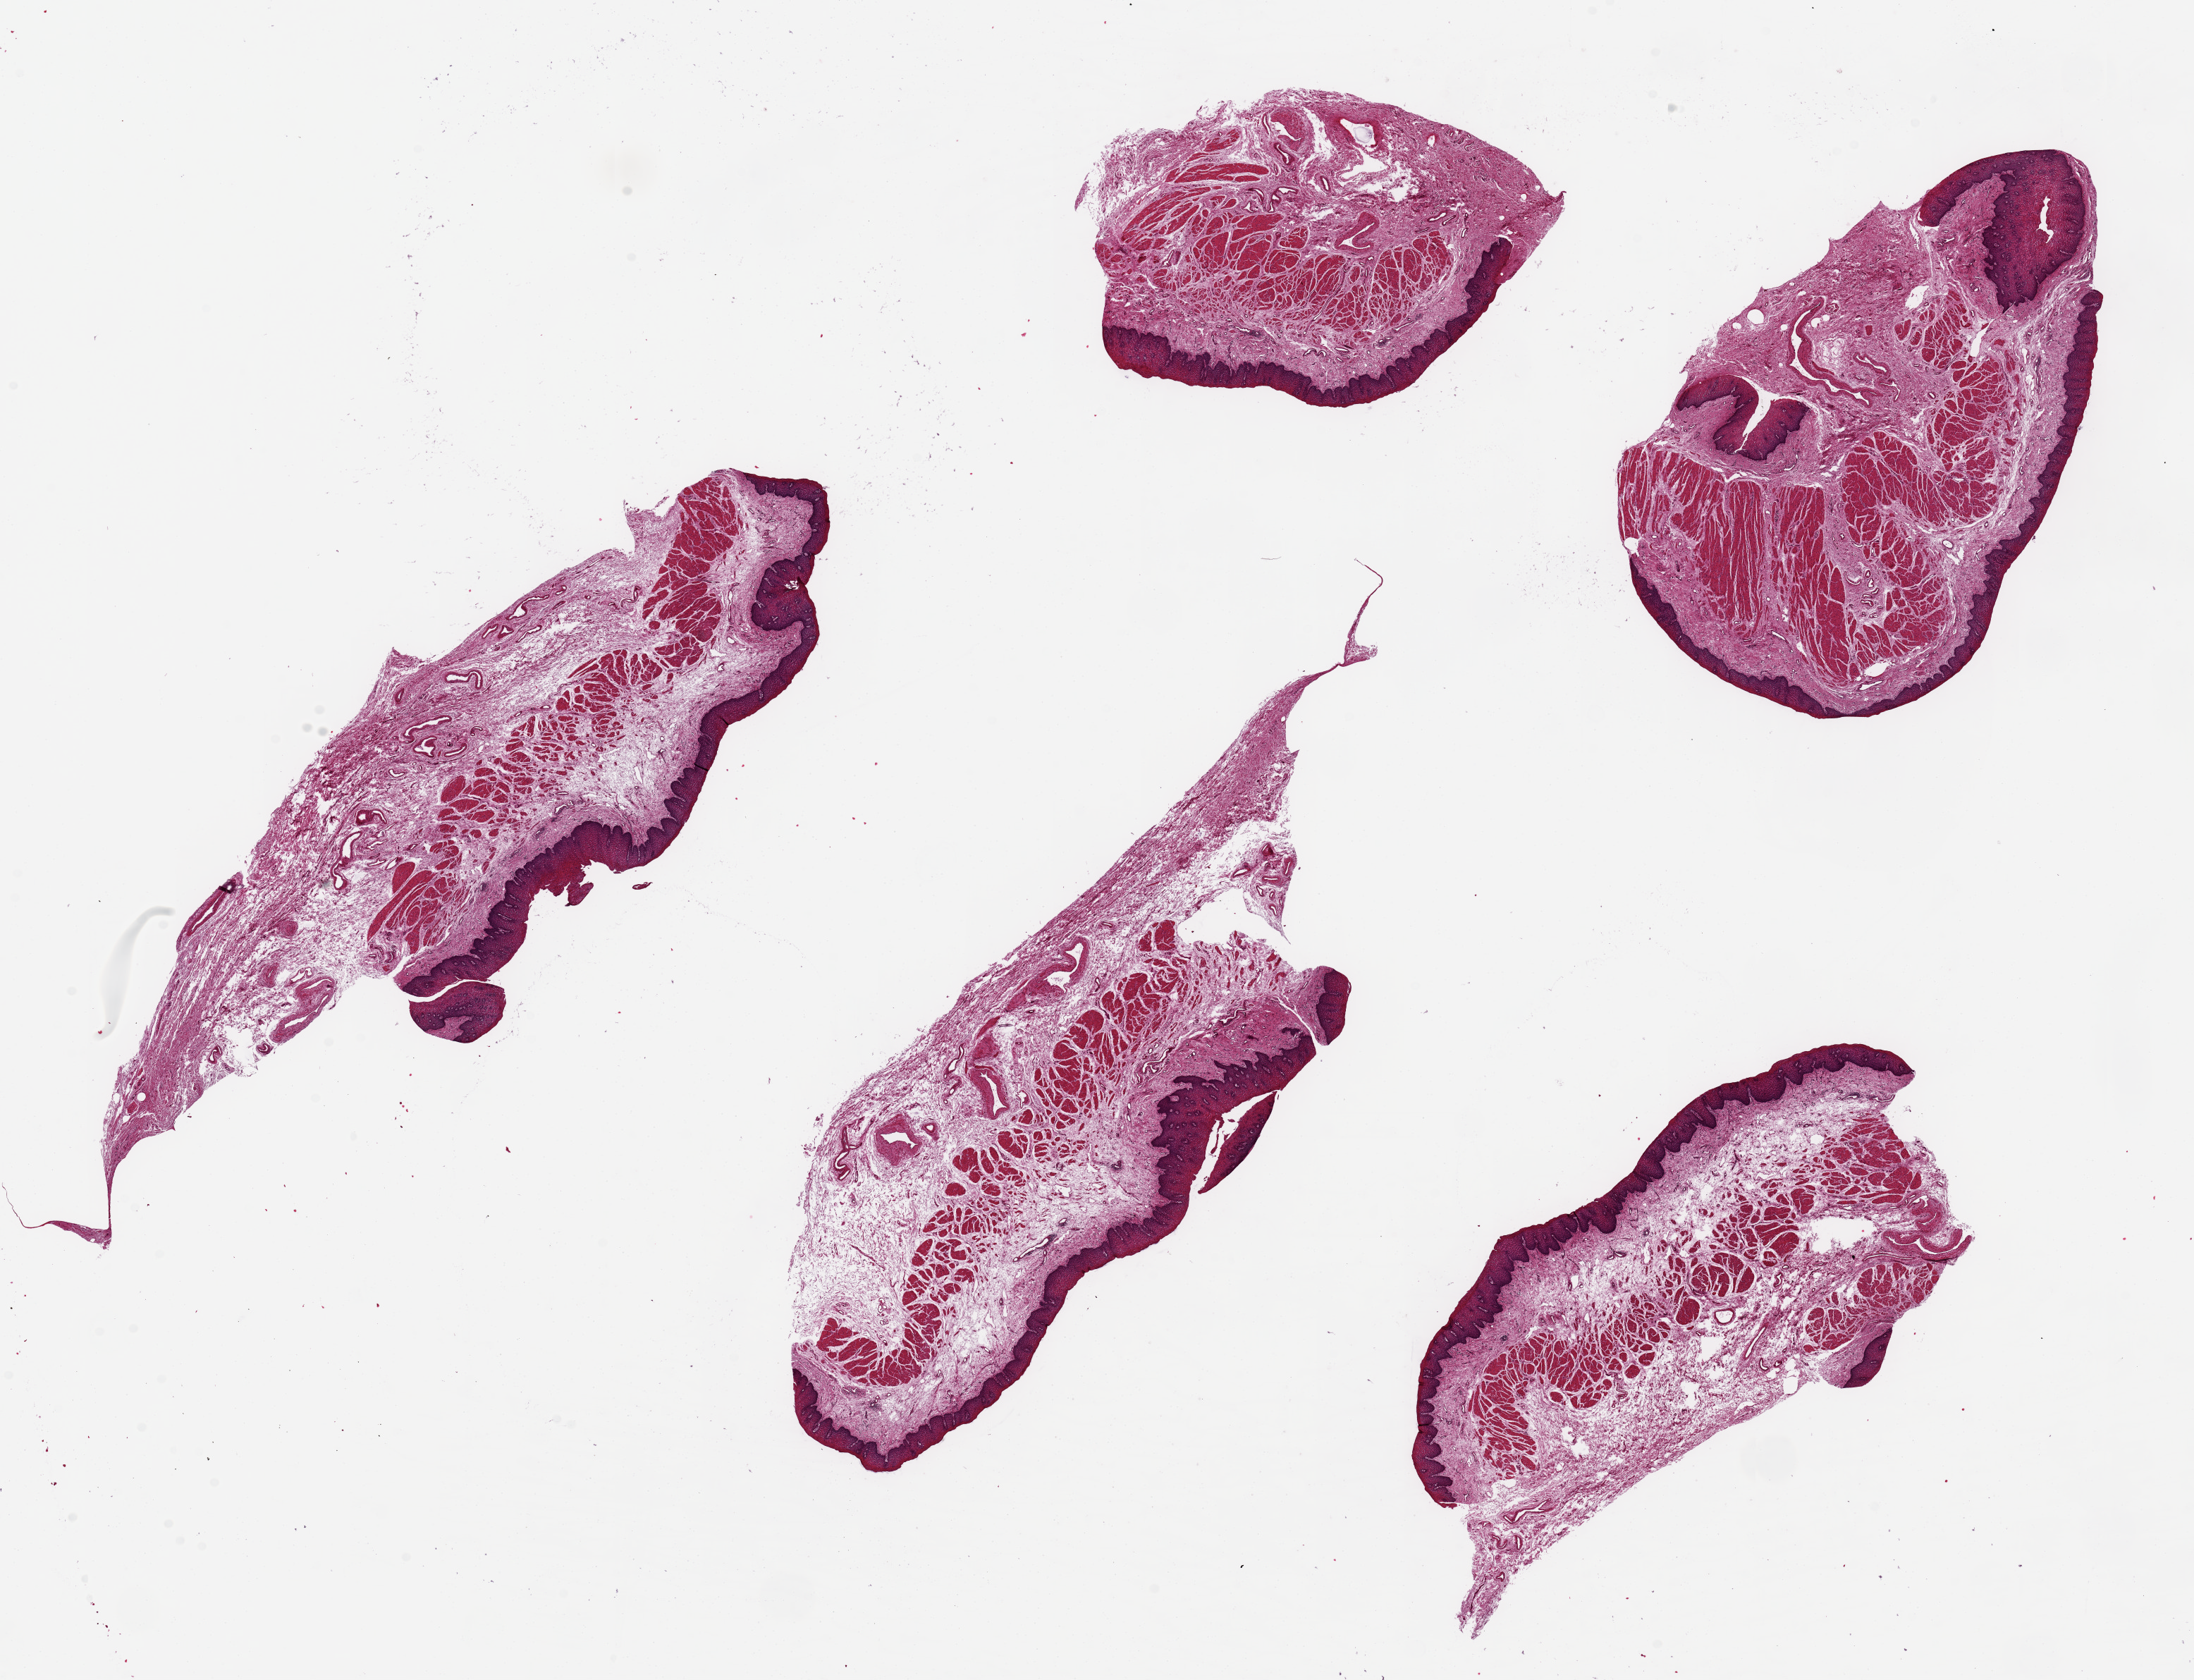
Whole-slide image, haematoxylin and eosin stain — shown as a low-resolution overview of the whole scanned area (about 24.6 x 18.8 mm, acquisition: 20x scan); PAXgene-fixed, paraffin-embedded tissue; sampled site (target tissue): esophageal mucous membrane; tissue donor sample. Female donor.
* review note (as recorded): 5 pieces ~7x3mm, all with good epithelium